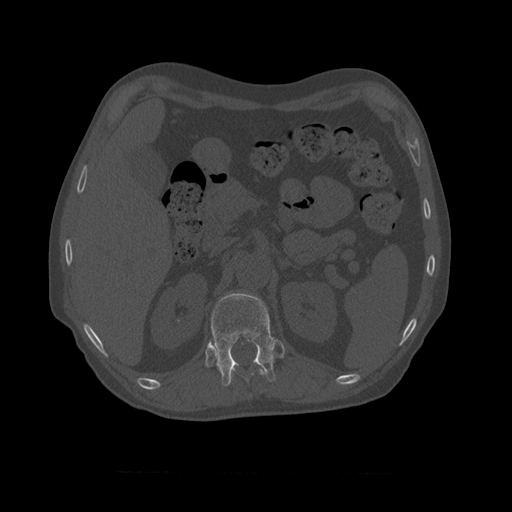
CT including the spine, one axial slice; slice 382 of 450 in the series (ordered by position); reconstruction kernel STANDARD; 120 kVp; bone window (W 1800 / L 400 HU); 1.25 mm slice thickness; 512 × 512 image matrix. Patient age 75 years. Case-level facts recorded for this patient, not image findings: primary cancer: prostate.
Annotated regions visible in this slice (semi-automatically segmented with operator editing):
- T10 vertebra: bounding box (x1, y1, x2, y2) in pixels: (229, 369, 264, 383)
- T11 vertebra: (209, 293, 276, 387)